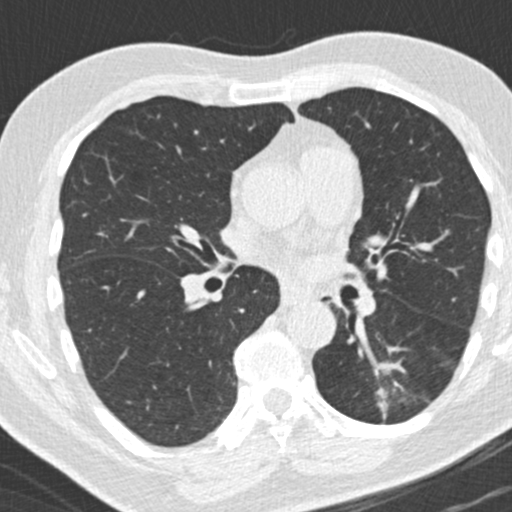
Low-dose screening chest CT, axial slice, third screening round (two years after baseline), lung window (W 1500 / L -600 HU), standard (soft-tissue) reconstruction kernel (B30f), 512 × 512 image matrix, field of view 300 × 300 mm. Male, age 66 years at enrolment. Former smoker at enrolment.
- Expert-annotated lung lesion, bounding box <357,355,425,426> (left, top, right, bottom; pixels).
- Reader record for this screening exam (exam-level; its link to the box is not recorded): non-calcified nodule or mass ≥4 mm, left lower lobe, 31 × 24 mm, spiculated (stellate) margins, pre-existing on the prior screen: yes; interval growth: yes.
- Lung cancer was diagnosed 56 days after this screen: adenocarcinoma, NOS, left lower lobe, poorly differentiated (G3), stage IB (AJCC 6th edition), 38 mm at pathology.